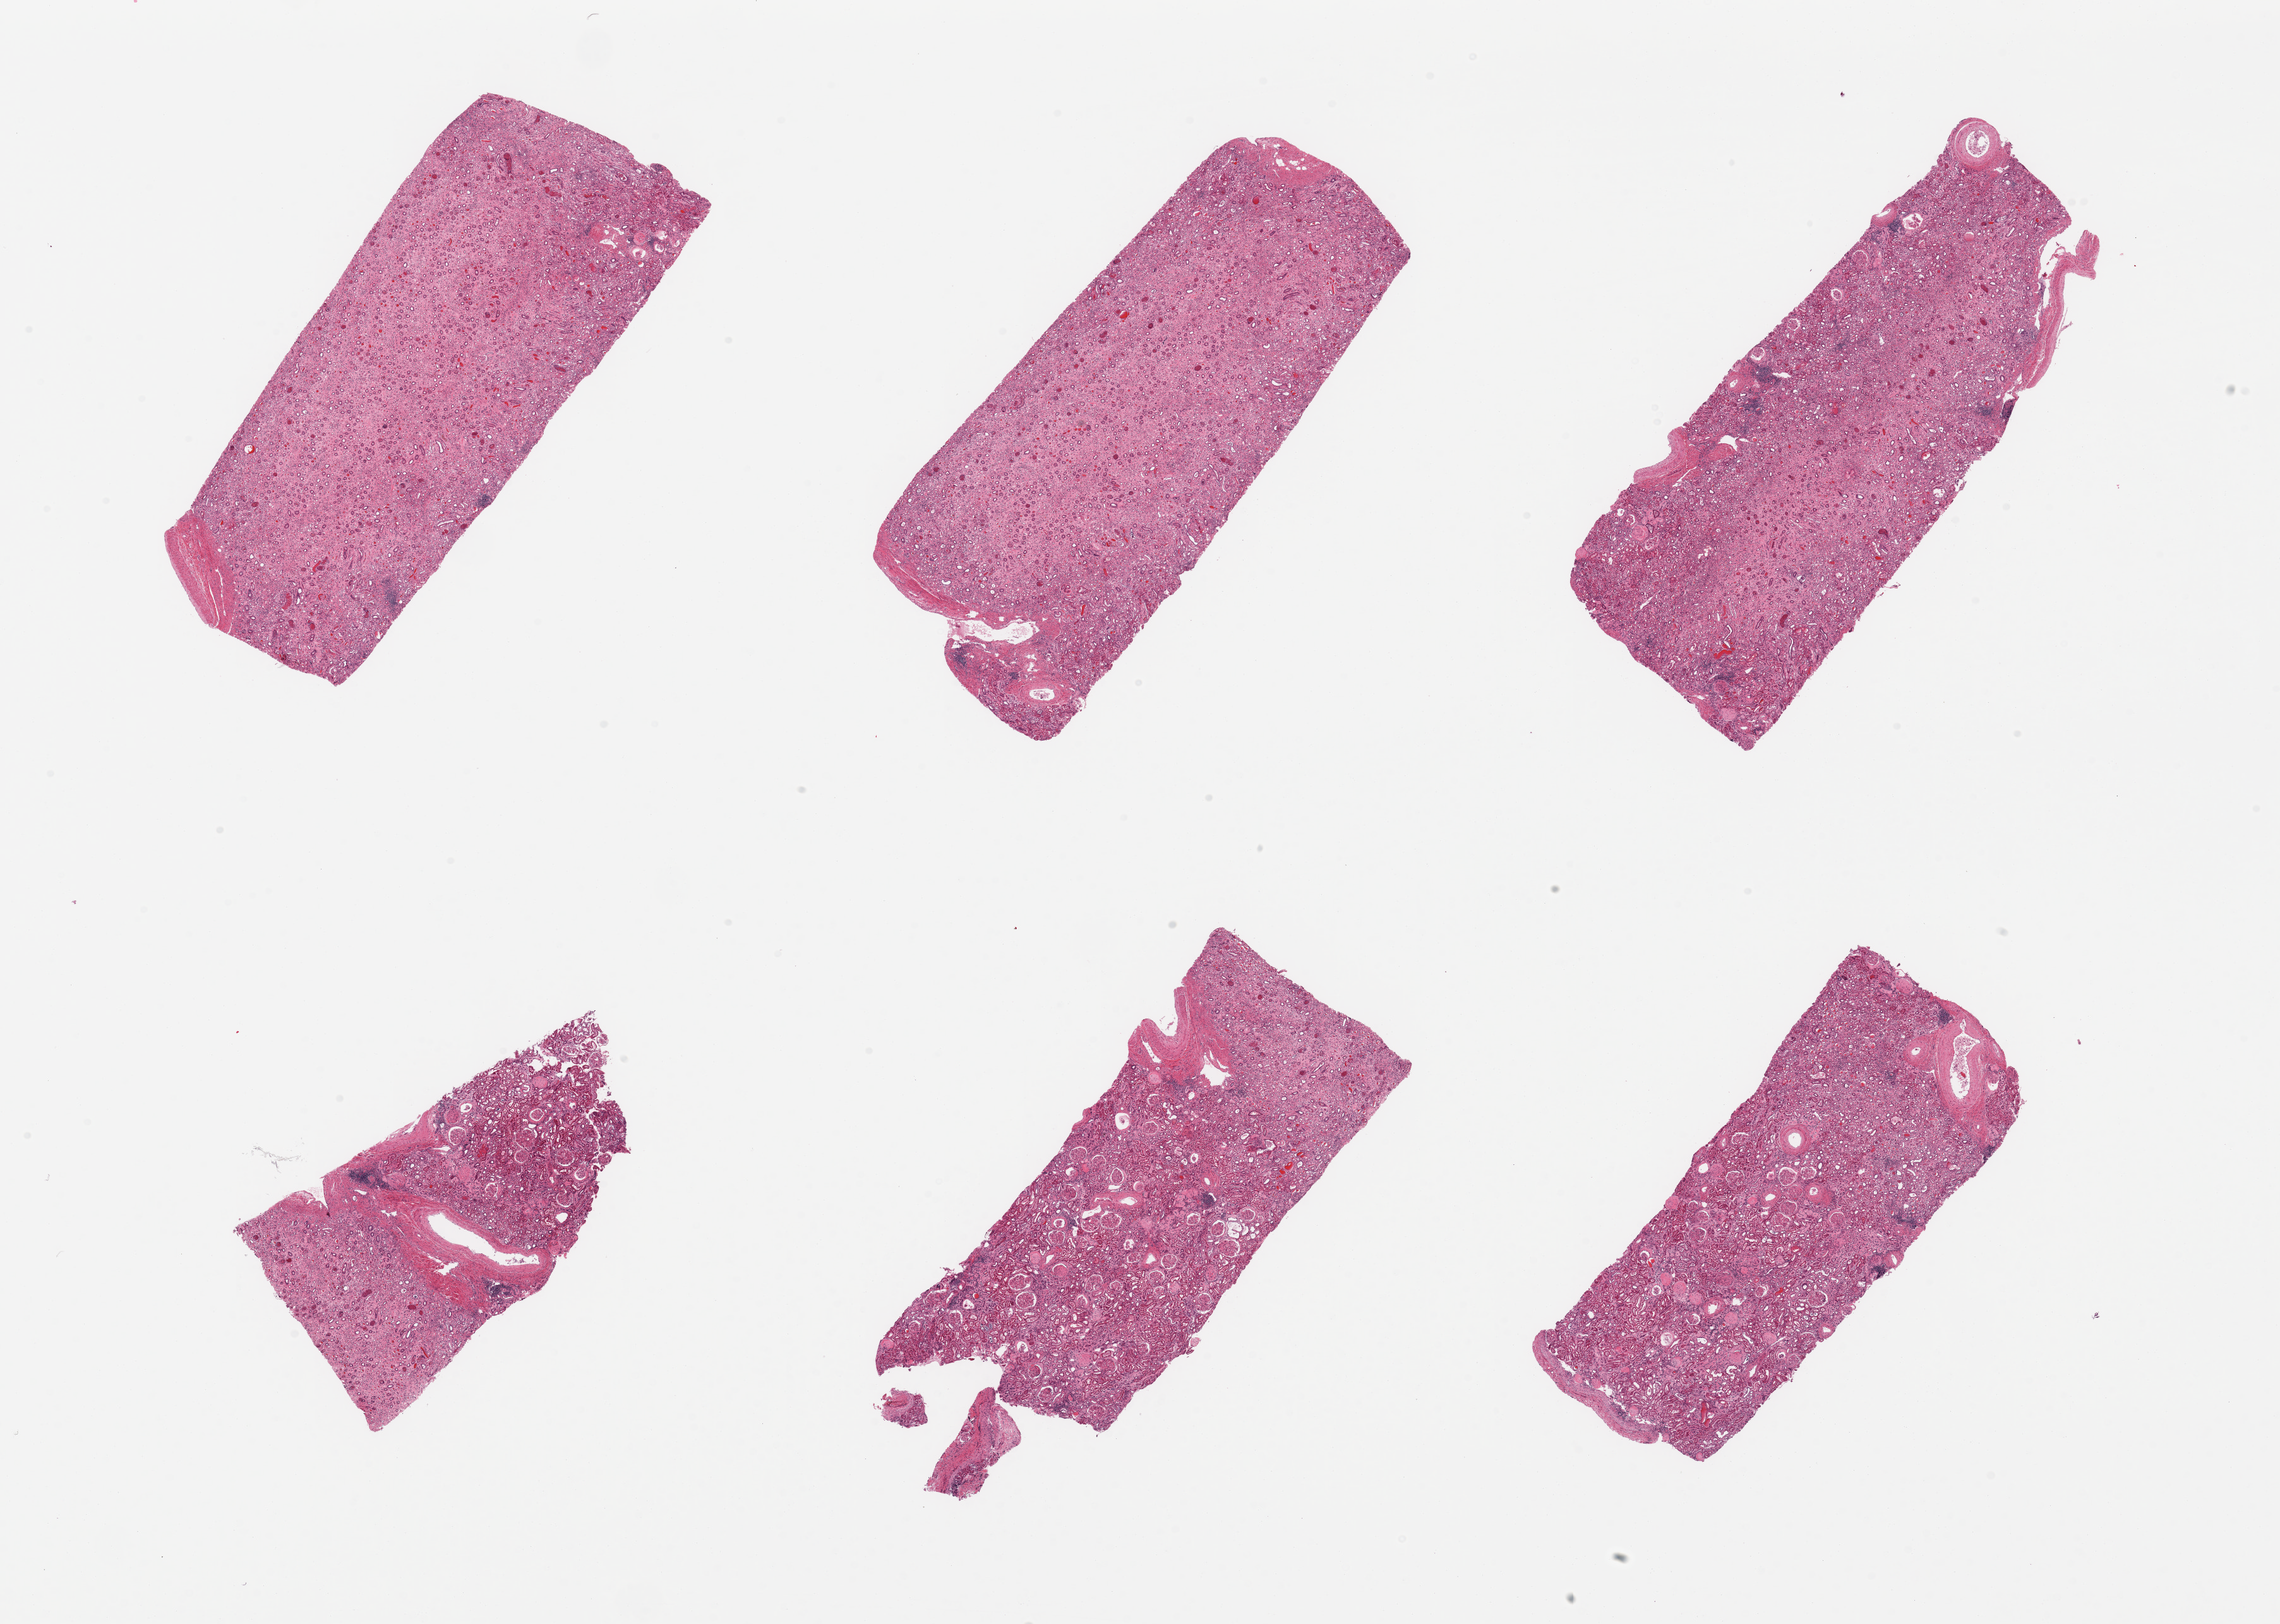
Hematoxylin and eosin (H&E) whole-slide image — shown as a low-resolution overview of the whole scanned area (about 28.5 x 20.3 mm), PAXgene-fixed, paraffin-embedded tissue, section of renal cortex (target tissue), donor tissue sample. Donor sex: female.
Reviewer comment on this tissue sample: 6 pieces; over half the pieces are largely medulla; considerable glomerular and vascular sclerosis.